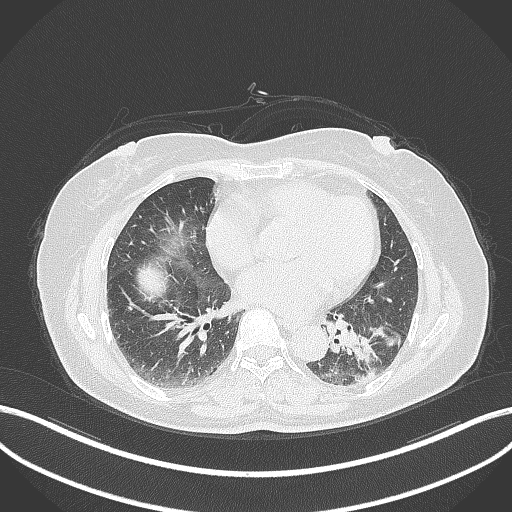
Chest CT, one axial slice; position 159 of 311 along the scan axis; lung window (W 1500 / L -600 HU); 1 mm slice thickness; 512 × 512 image matrix. Patient: female, 59 years. From the clinical record (not read from this slice): clinical TNM (as recorded): T2a N0 M0.
Annotated regions visible in this slice (rectangle marked by the reading radiologist):
- lung tumour (recorded histology: adenocarcinoma): bounding box (x1, y1, x2, y2) in pixels: (336, 319, 383, 368)